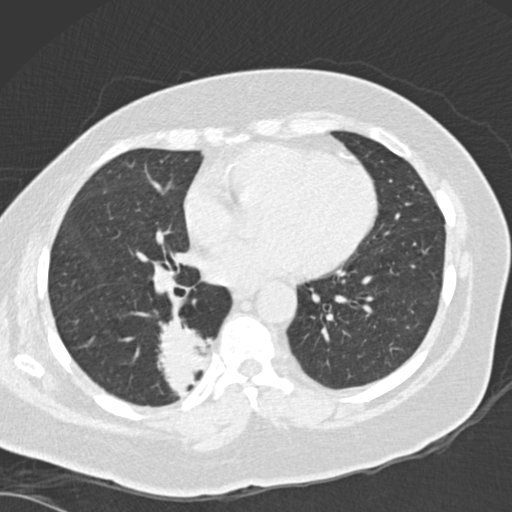
Chest CT (low-dose screening protocol), one axial image, first (baseline) screen, lung window (W 1500 / L -600 HU), slice 94 of 162 in the series. Female participant, aged 66 years at enrolment.
Expert reader's lesion annotation, bounding box [x1, y1, x2, y2] px = [151, 321, 226, 398]. The screening reader recorded 3 non-calcified nodules or masses ≥4 mm on this exam; which of them this box marks is not recorded. Official screen result: positive, change unspecified: nodule(s) >= 4 mm or enlarging nodule(s), mass(es), or other non-specific abnormalities suspicious for lung cancer. Participant outcome: lung cancer diagnosed 67 days after this screen — adenocarcinoma, NOS, right lower lobe, well differentiated (G1), stage IB (AJCC 6th edition), 55 mm at pathology.